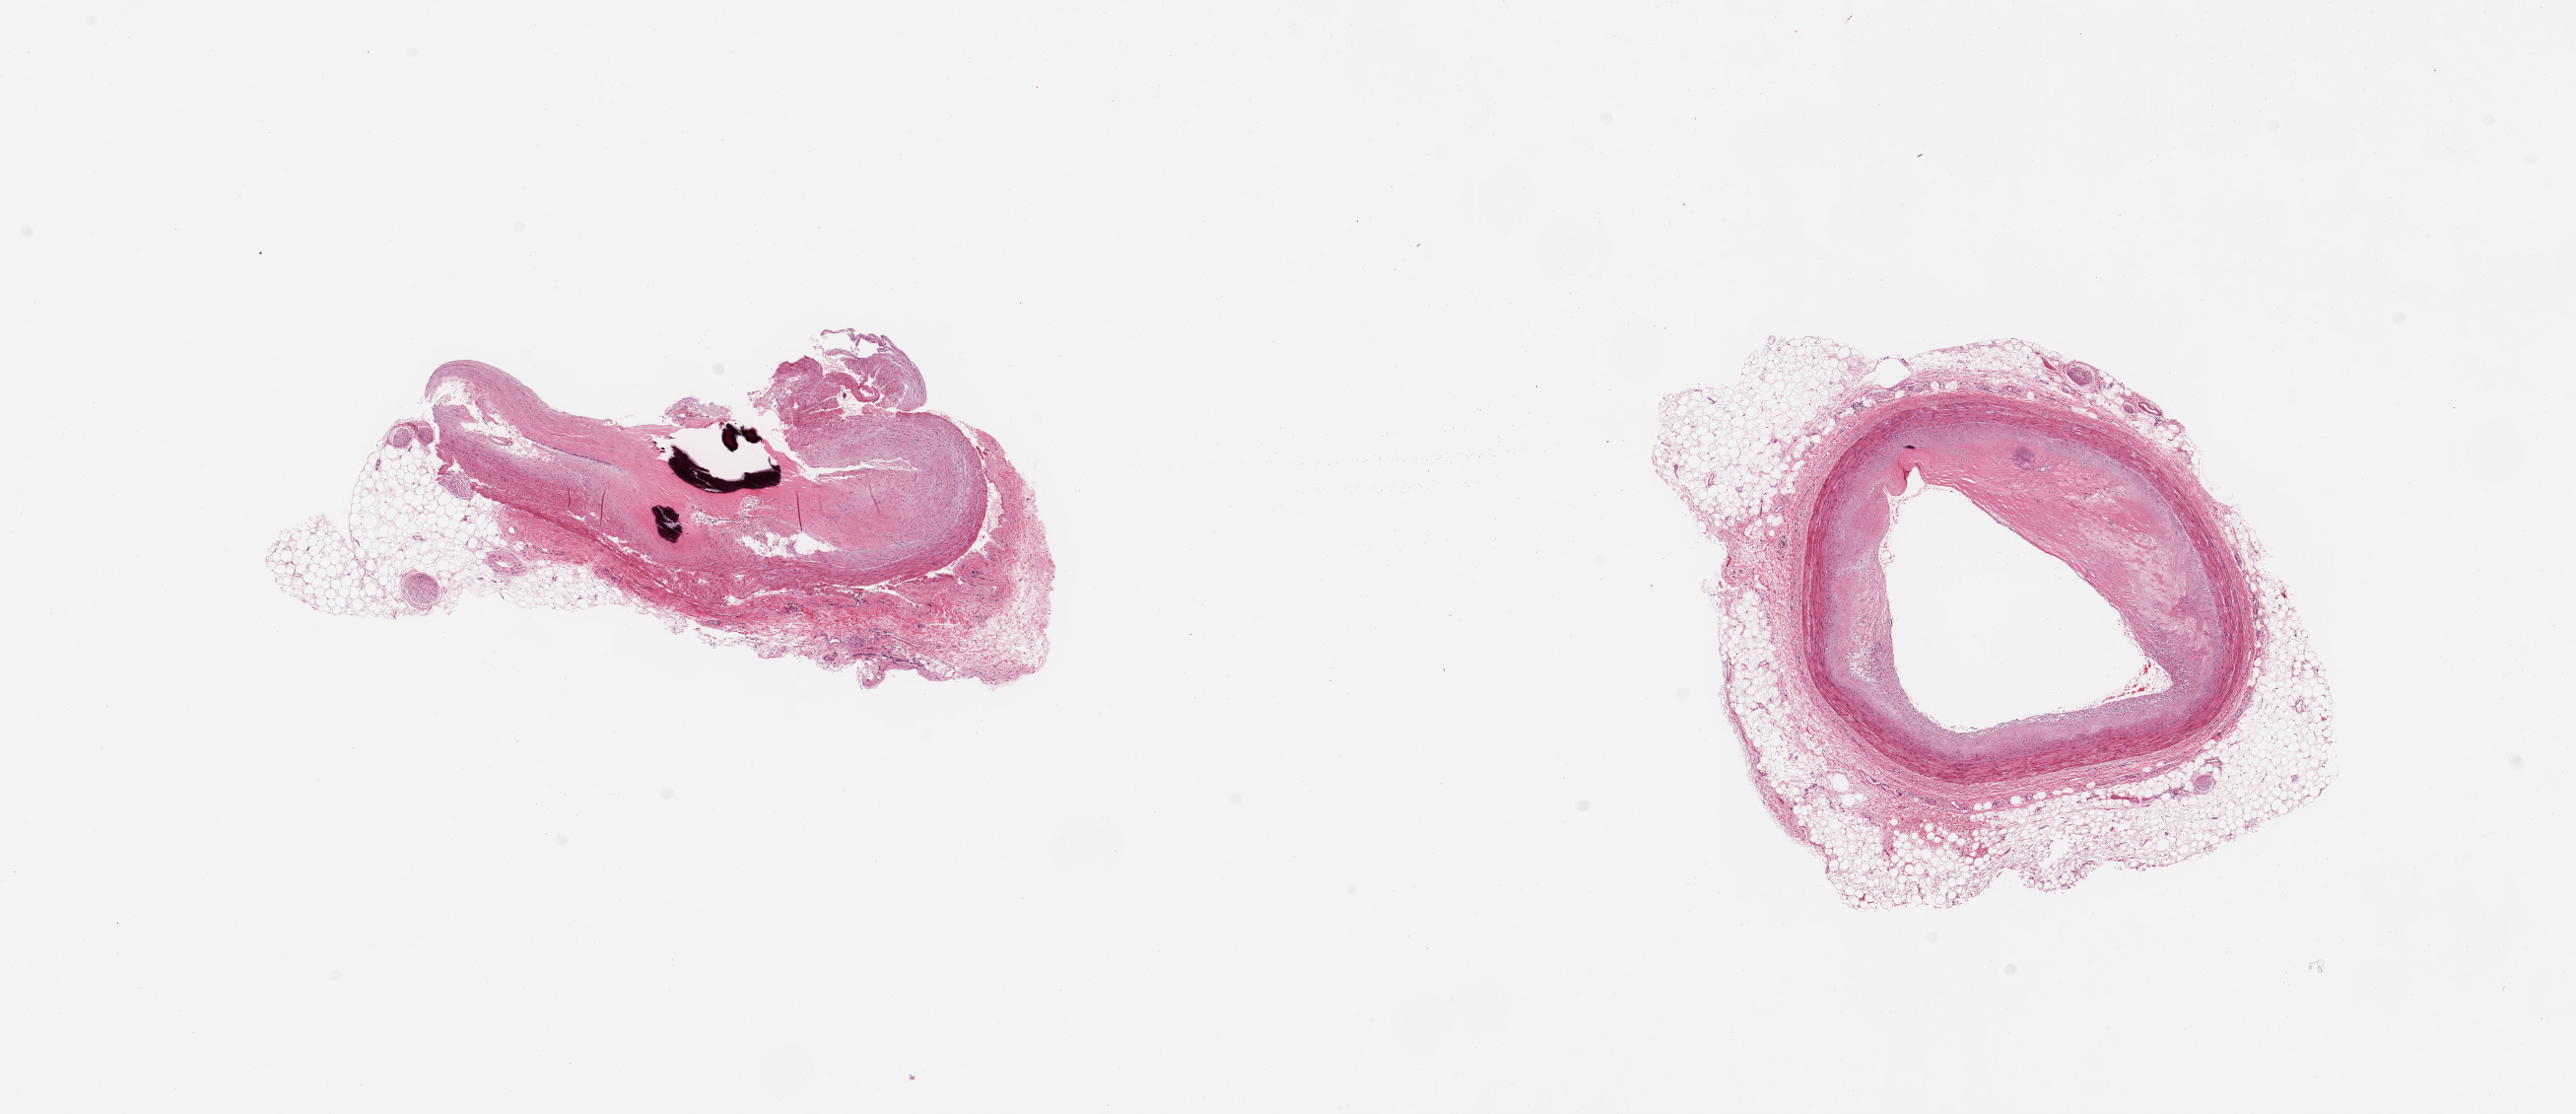
Digitized hematoxylin and eosin (H&E)-stained section — a low-resolution overview of the entire scanned area, about 20.7 x 8.9 mm (from a 20x scan); PAXgene-fixed paraffin-embedded (PFPE) section; sampled site (target tissue): coronary artery; tissue donor sample. Donor sex: male.
Reviewer comment on this tissue sample: 2 pieces; large atherosclerotic plaques, 1 calcified; untrimmed external fat.